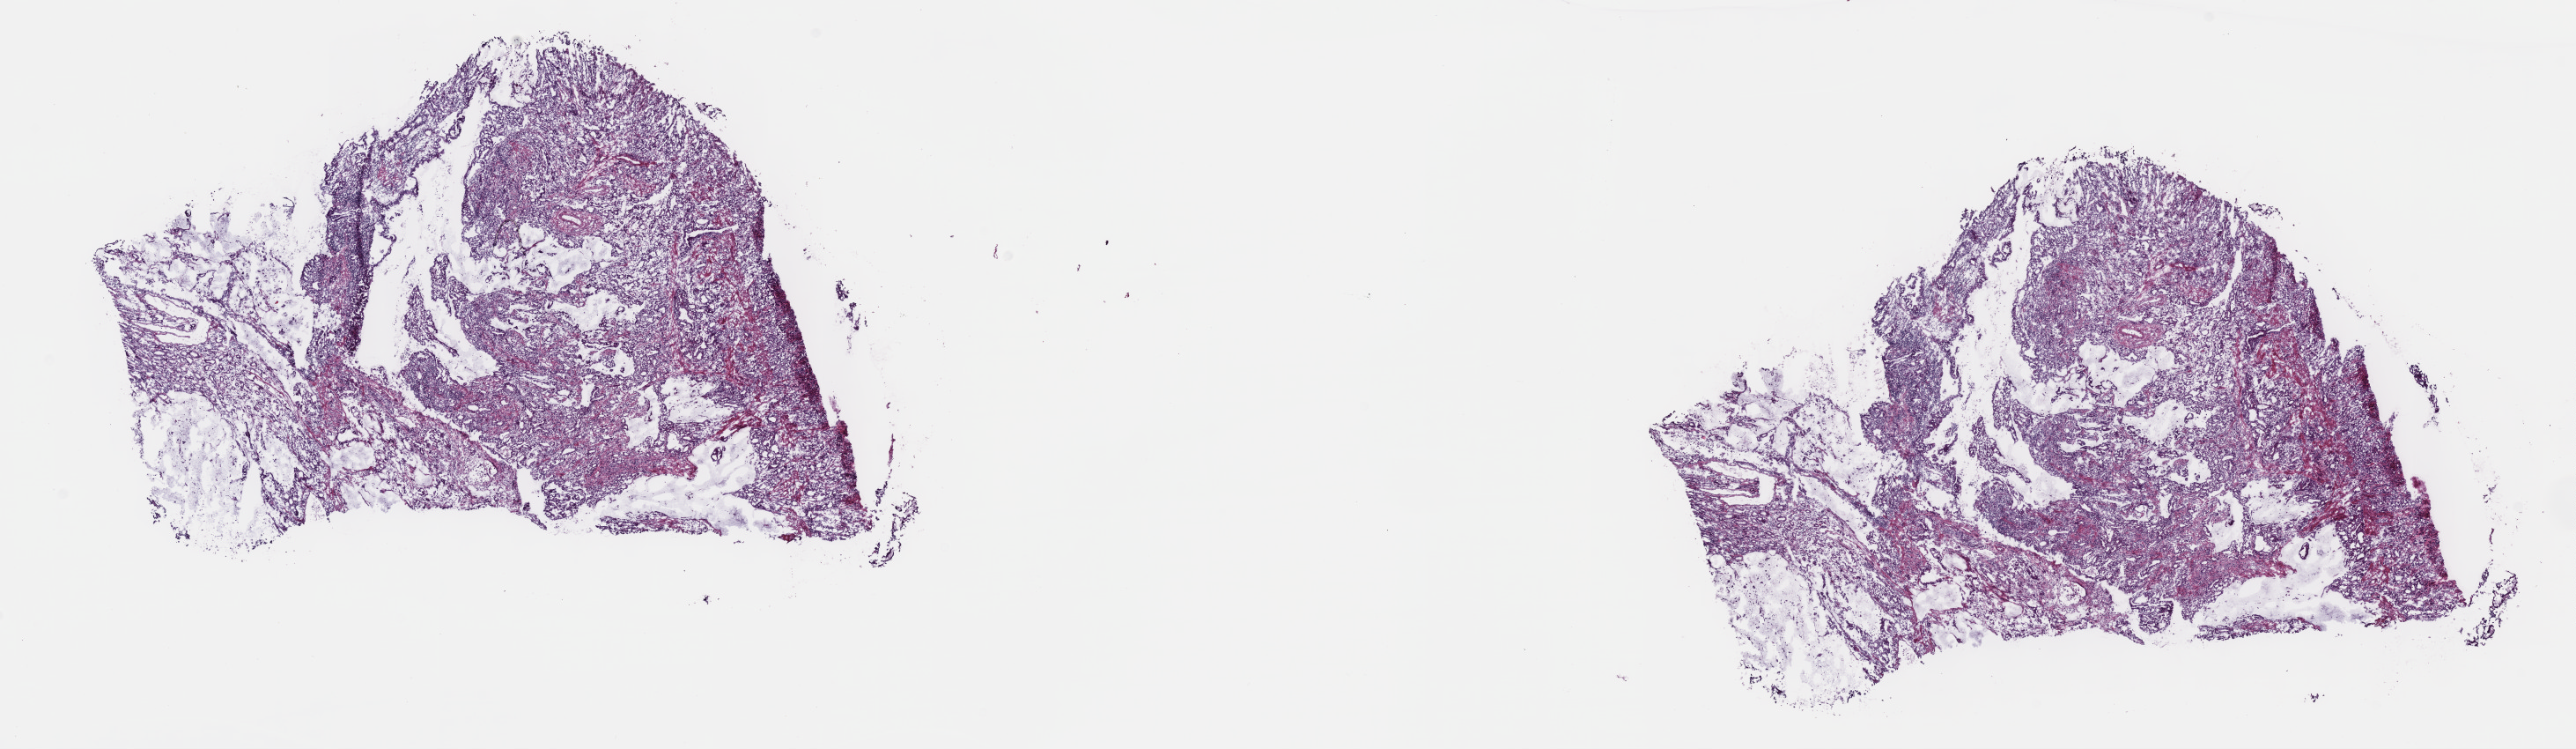
H&E-stained whole-slide image, whole scanned area (about 23.7 x 6.9 mm, acquisition: 40x scan) shown as a low-resolution overview, frozen section from the top of the tissue portion, primary tumour sample from the stomach. Patient: male, age at initial diagnosis 59 years. Pathologist review of this section (percent, as recorded): tumour cells 75%, tumour nuclei 60%.
Pathologic diagnosis: Signet ring cell carcinoma (cardia, NOS).